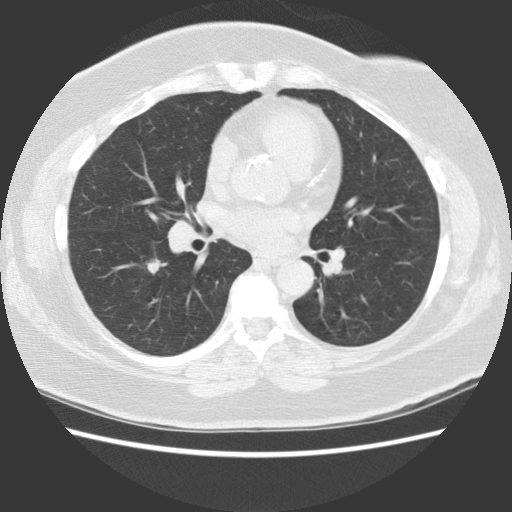
Low-dose screening chest CT, one axial slice; slice 57 of 117 in the series (ordered by position); lung window (W 1500 / L -600 HU); 2.5 mm slice thickness; 512 × 512 image matrix.
Structures marked on this image (outlined manually by an expert reader):
- lesion 1 (tumor, lower lobe of right lung): bounding box [x1, y1, x2, y2] px = [146, 258, 165, 274]